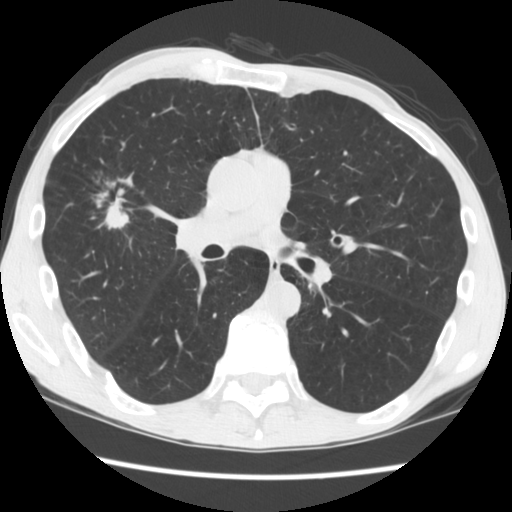
Axial slice from a low-dose chest CT screening exam, second annual screen, lung window (W 1500 / L -600 HU), 2.5 mm slice thickness, standard (soft-tissue) reconstruction kernel (STANDARD), 120 kVp, 512 × 512 image matrix. Male participant, aged 56 years at enrolment.
- Expert reader's lesion annotation, box from (x=82, y=158) to (x=146, y=232) px.
- The screening reader recorded 2 non-calcified nodules or masses ≥4 mm on this exam (right upper lobe, left upper lobe); which of them this box marks is not recorded.
- Official screen result: positive, change unspecified: nodule(s) >= 4 mm or enlarging nodule(s), mass(es), or other non-specific abnormalities suspicious for lung cancer.
- Lung cancer was diagnosed 101 days after this screen: squamous cell carcinoma, NOS, right upper lobe, right middle lobe, well differentiated (G1), stage IA (AJCC 6th edition), 27 mm at pathology.